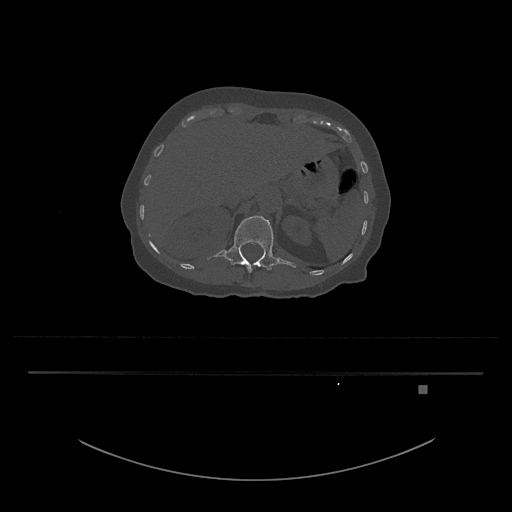
CT including the spine, one axial slice. Position 557 of 797 along the scan axis. Reconstruction kernel Br40s/3. Bone window (W 1800 / L 400 HU). 512 × 512 image matrix, field of view 500 × 500 mm. Patient: female, 57 years. Case-level facts recorded for this patient, not image findings: primary cancer: cervical.
Outlined on this slice (semi-automatically segmented with operator editing):
- L1 vertebra: bounding box [x1, y1, x2, y2] px = [207, 216, 296, 273]